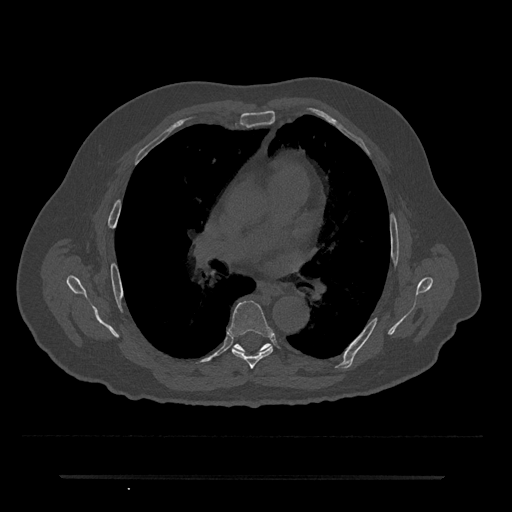
CT including the spine, one axial slice; slice 423 of 797 in the series (ordered by position); reconstruction kernel Br40s/3; bone window (W 1800 / L 400 HU); 0.5 mm slice thickness; 512 × 512 image matrix, field of view 437 × 437 mm. Male patient, age 69 years. From the clinical record (not read from this slice): primary cancer: prostate.
Outlined on this slice (semi-automatically segmented with operator editing):
- T6 vertebra: box from (x=229, y=300) to (x=274, y=369) px
- T7 vertebra: (x=233, y=344)–(x=270, y=350)